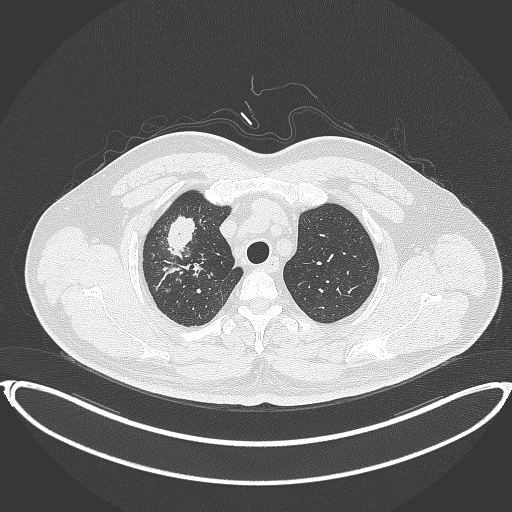
Chest CT, one axial slice; position 321 of 399 along the scan axis; reconstruction kernel B70f; 120 kVp; lung window (W 1500 / L -600 HU); 1 mm slice thickness; 512 × 512 image matrix, field of view 445 × 445 mm. Male patient, age 53 years. Case-level facts recorded for this patient, not image findings: clinical TNM (as recorded): T2a N0 M0.
Annotated regions visible in this slice (rectangle marked by the reading radiologist):
- lung tumour (recorded histology: adenocarcinoma): bounding box (x1, y1, x2, y2) in pixels: (162, 213, 200, 258)